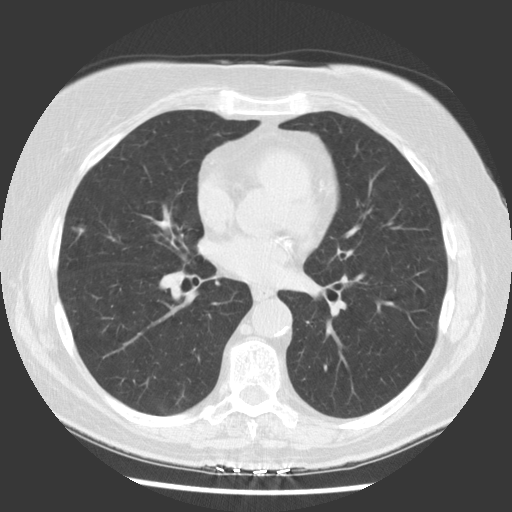
Low-dose screening chest CT, one axial slice; position 77 of 142 along the scan axis; reconstruction kernel STANDARD; 140 kVp; lung window (W 1500 / L -600 HU); 2.5 mm slice thickness; 512 × 512 image matrix, field of view 340 × 340 mm.
Annotated regions visible in this slice (expert manual segmentation):
- lesion 1 (tumor, middle lobe of right lung): bounding box (x1, y1, x2, y2) in pixels: (79, 228, 84, 236)